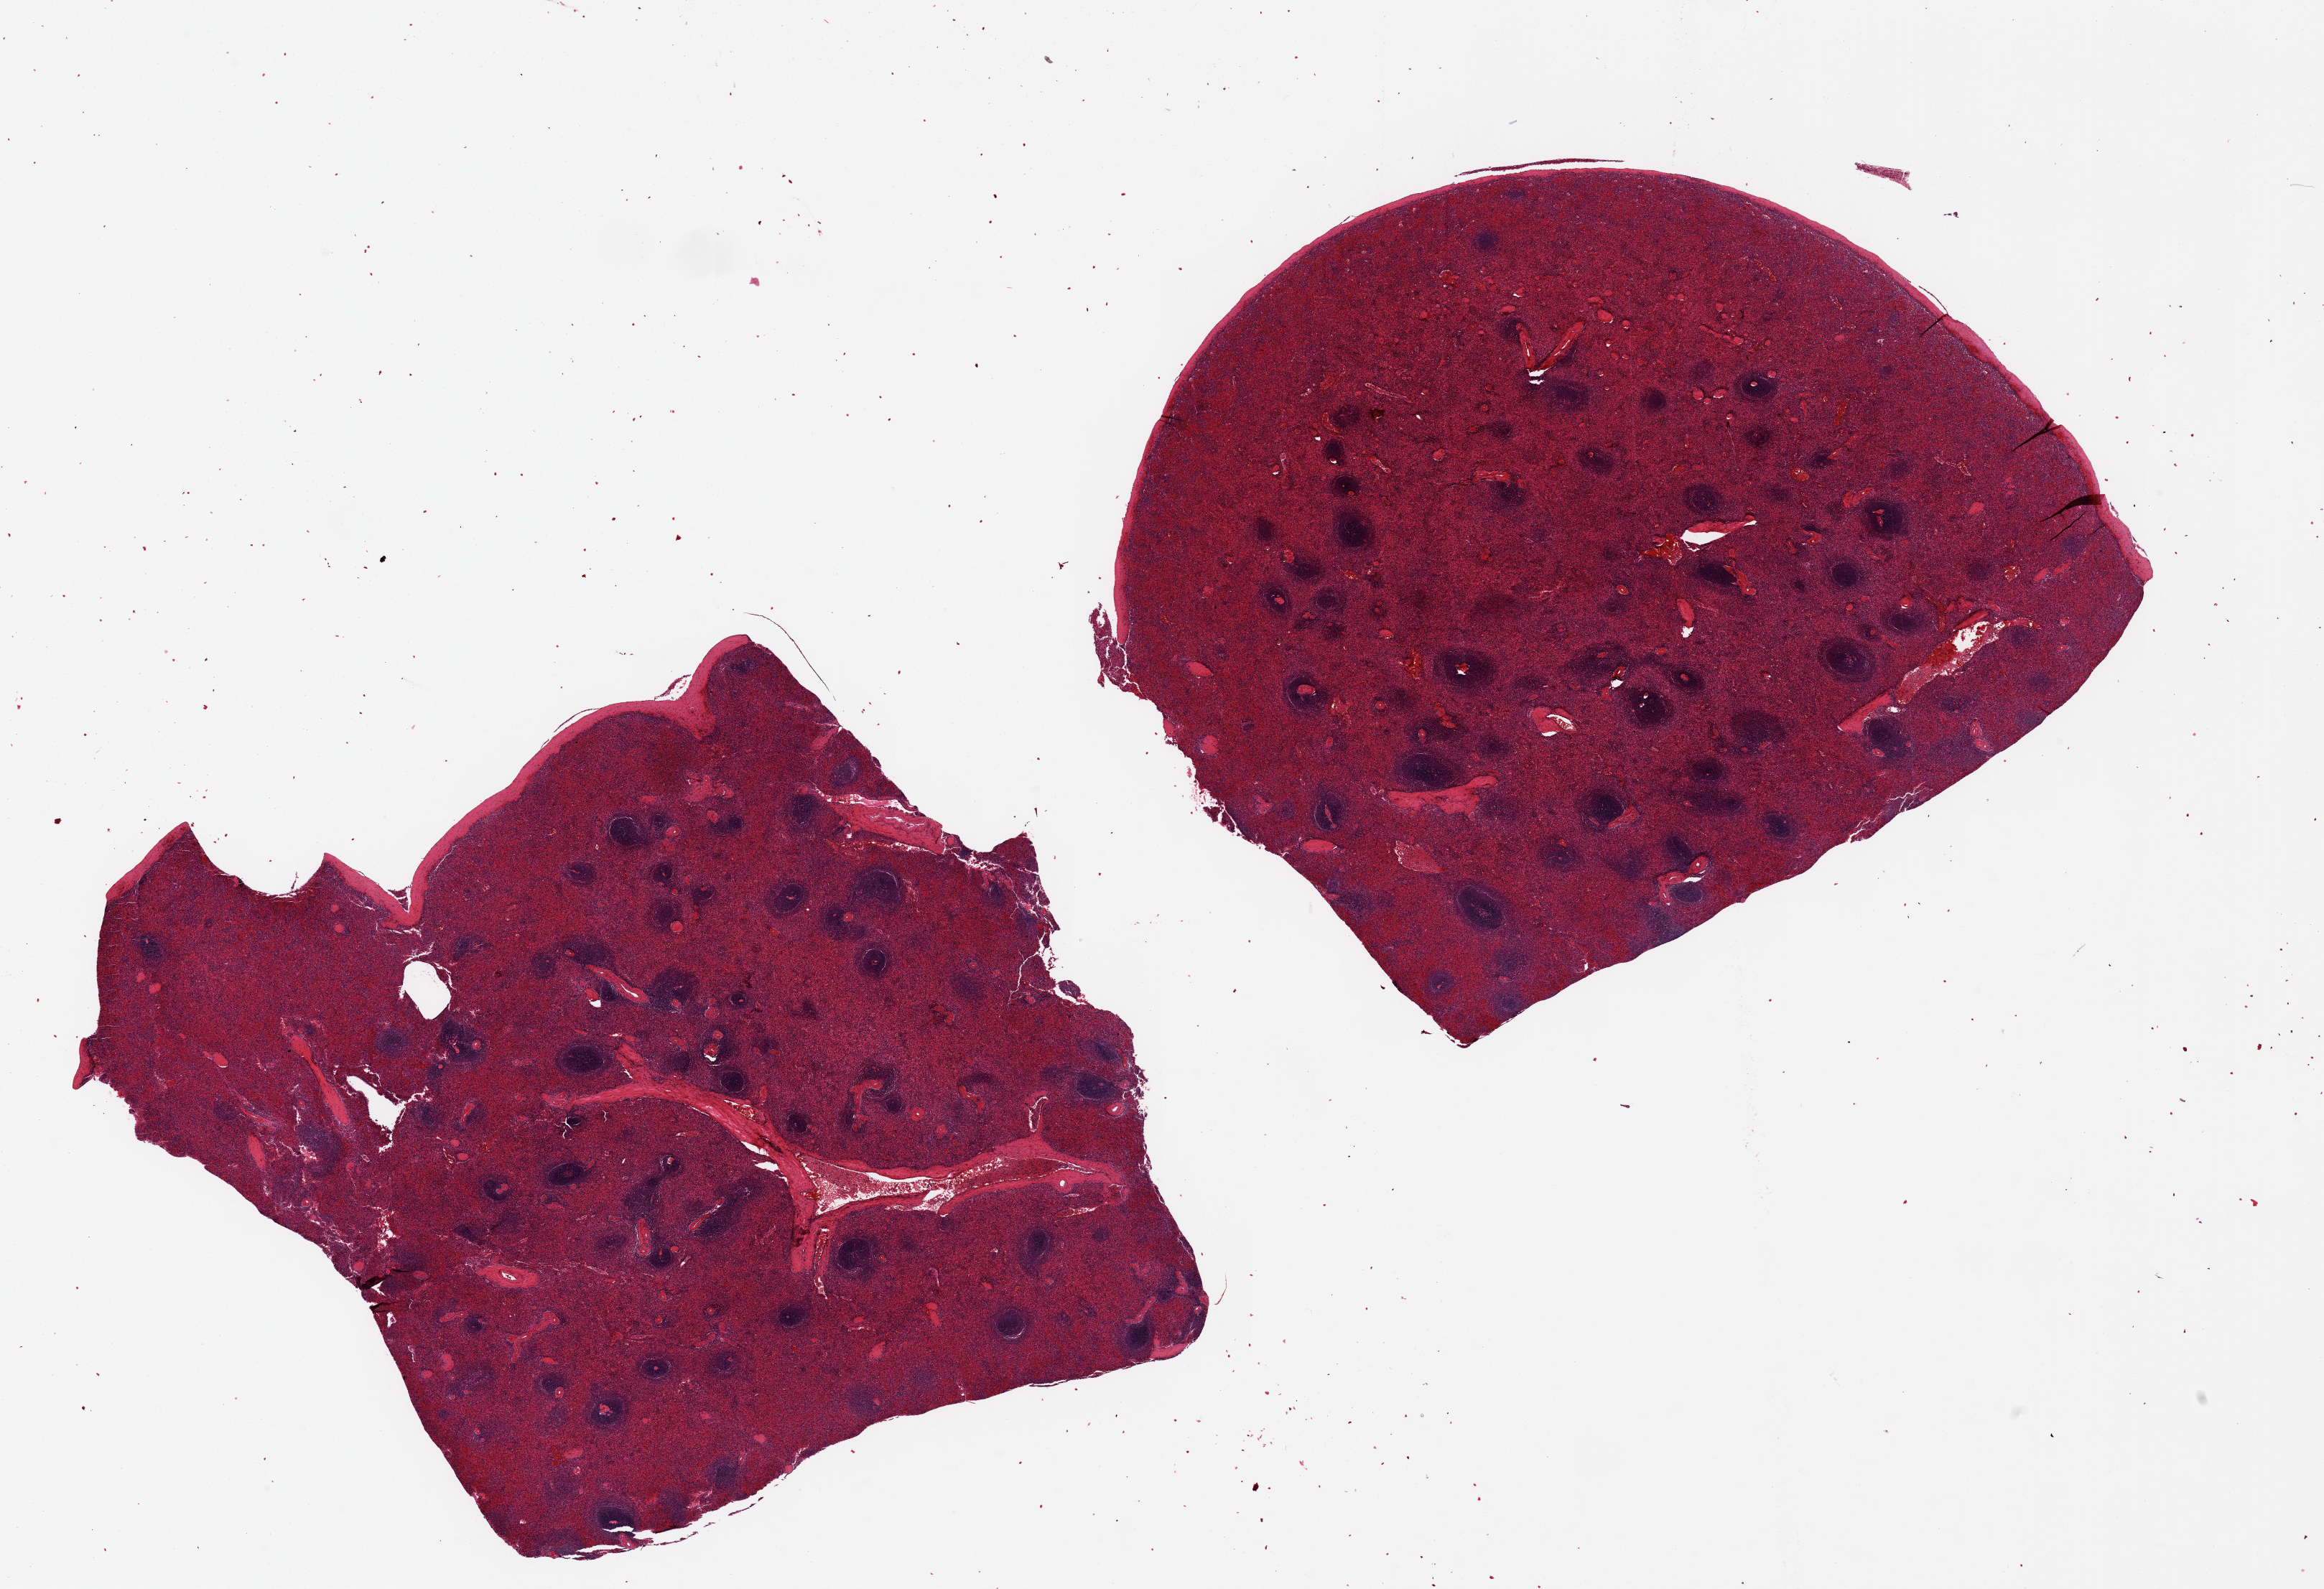
Digitized hematoxylin and eosin (H&E)-stained section, brightfield, low-resolution overview of the scanned area, about 25.6 x 17.5 mm (from a 20x scan), PAXgene-fixed, paraffin-embedded tissue, section of spleen (target tissue), tissue donor sample. Donor sex: female.
Reviewer comment on this tissue sample: 2 pieces 9x8 & 9x8 mm; moderate congestion.